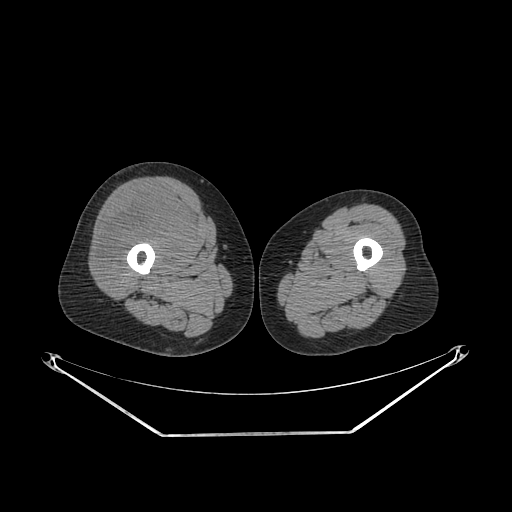
CT of an extremity soft-tissue mass (from a PET/CT study), one axial slice; position 239 of 311 along the scan axis; reconstruction kernel SOFT; soft-tissue window (W 400 / L 40 HU); 3.75 mm slice thickness; 512 × 512 image matrix. Female patient. From the clinical record (not read from this slice): histological type: pleiomorphic undifferentiated sarcoma; grade: high; site of the primary tumour: right quadricep.
Structures marked on this image (expert contour drawn on MRI and transferred to this co-registered scan by the dataset authors):
- tumour plus oedema (research contour): bounding box <100,192,186,279> (left, top, right, bottom; pixels)
- tumour (research contour): <100,192,186,279>